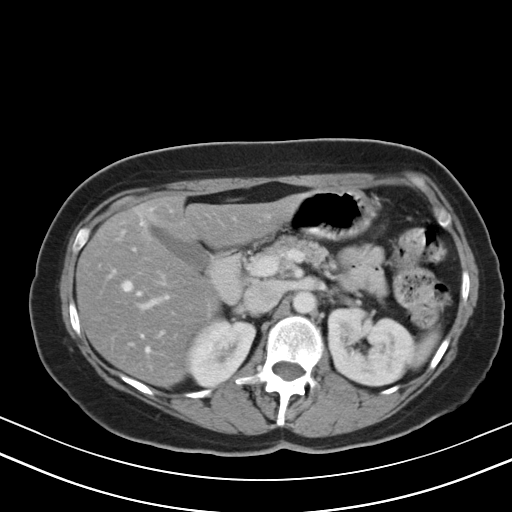
Contrast-enhanced abdominal CT, one axial slice. Slice 26 of 47 in the series (ordered by position). Reconstruction kernel B40s. 130 kVp. Intravenous contrast given. Soft-tissue window (W 400 / L 40 HU). 5 mm slice thickness. 512 × 512 image matrix, field of view 350 × 350 mm. Female patient. From the clinical record (not read from this slice): diagnosis: colorectal cancer liver metastases, imaged before liver resection; multiple liver metastases: no; largest metastasis: 3.5 cm; disease in both lobes: no.
Structures marked on this image (outlined manually by an expert reader):
- hepatic veins: box from (x=123, y=208) to (x=151, y=351) px
- liver: (x=77, y=195)–(x=297, y=386)
- planned liver remnant (the part of the liver to remain after resection): (x=77, y=195)–(x=297, y=386)
- portal vein (with intrahepatic branches): (x=137, y=280)–(x=171, y=311)